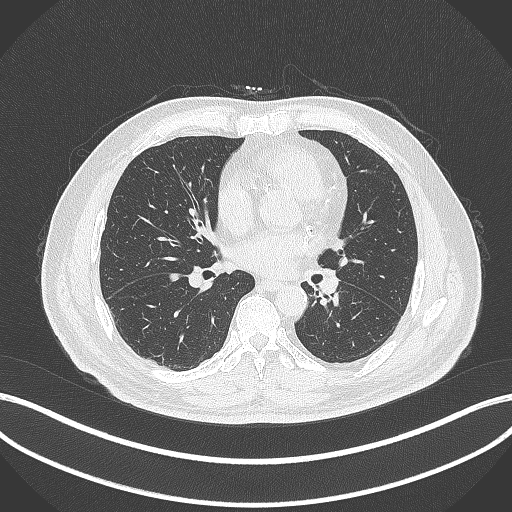
Chest CT, one axial slice; position 134 of 312 along the scan axis; reconstruction kernel B70f; 120 kVp; lung window (W 1500 / L -600 HU); 1 mm slice thickness; 512 × 512 image matrix, field of view 400 × 400 mm. Patient: male, 71 years. From the clinical record (not read from this slice): clinical TNM (as recorded): T1b N0 M0.
Annotated regions visible in this slice (rectangle marked by the reading radiologist):
- lung tumour (recorded histology: squamous cell carcinoma): bounding box <317,270,343,297> (left, top, right, bottom; pixels)